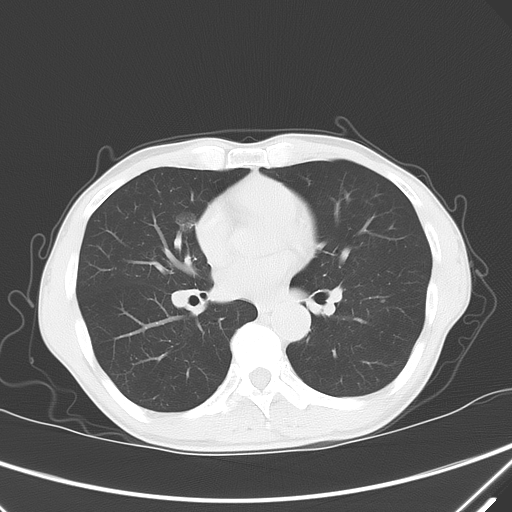
Chest CT, one axial slice; position 33 of 68 along the scan axis; 120 kVp; lung window (W 1500 / L -600 HU); 5 mm slice thickness; 512 × 512 image matrix, field of view 350 × 350 mm. Patient: male, 67 years. Case-level facts recorded for this patient, not image findings: clinical TNM (as recorded): T1c N0 M0; histopathological grade: G1-2.
Structures marked on this image (bounding box drawn by a radiologist):
- lung tumour (recorded histology: adenocarcinoma): bounding box [x1, y1, x2, y2] px = [171, 203, 198, 242]